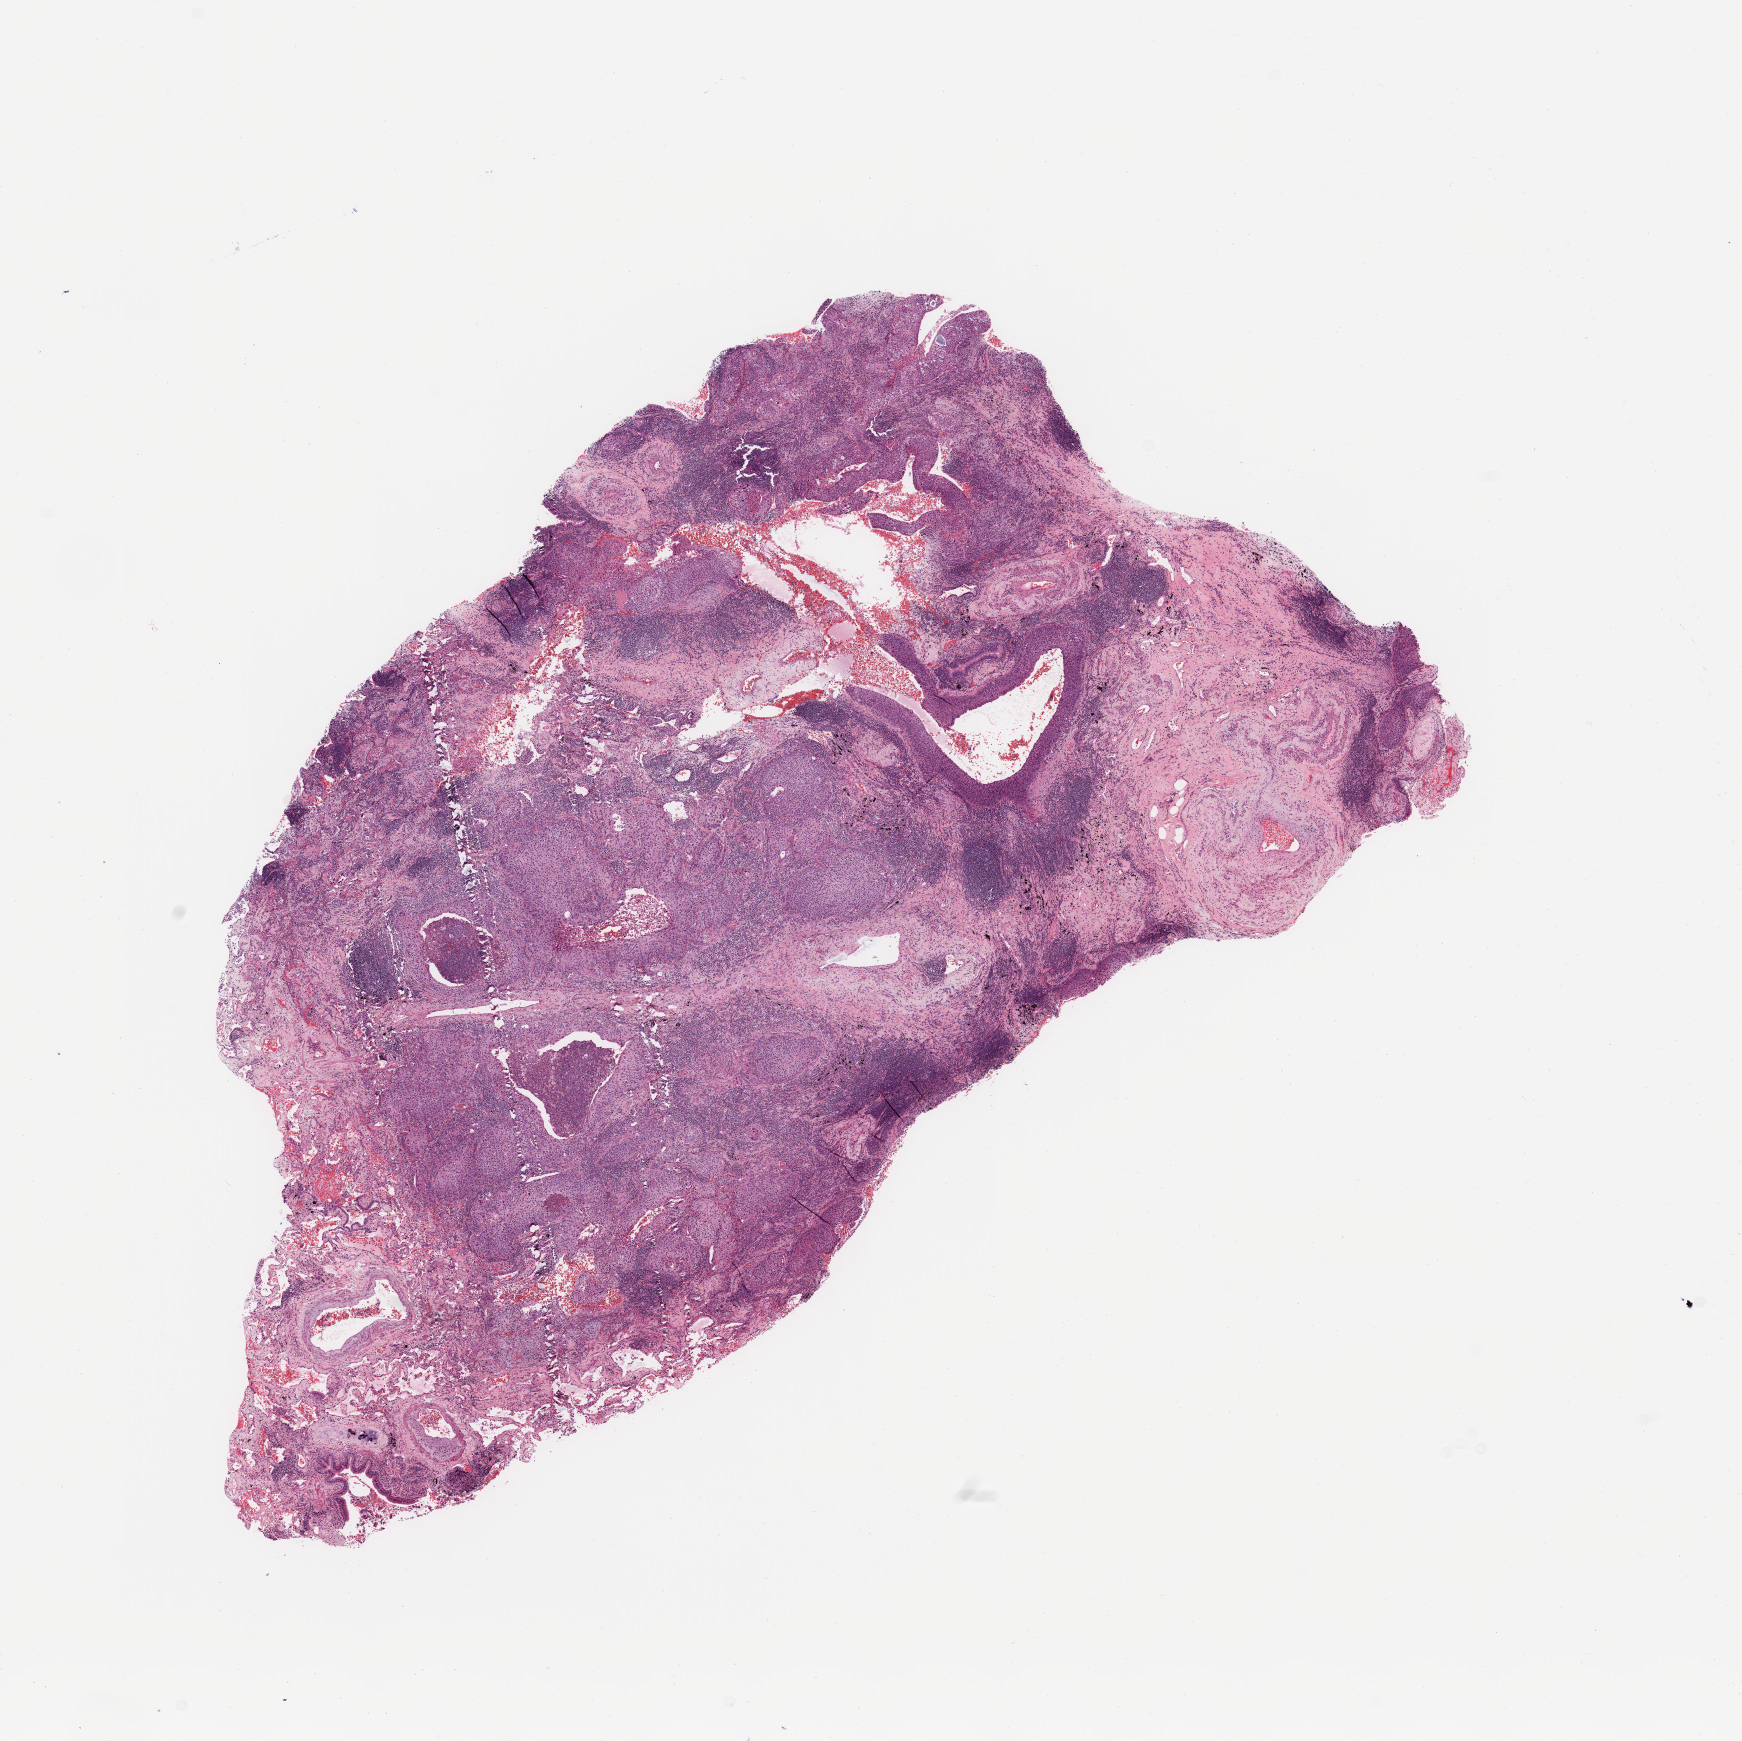
Whole-slide histology image, H&E-stained — shown as a low-resolution overview of the whole scanned area (about 13.8 x 13.8 mm), tumour tissue sample, sampled site: lung. 71-year-old female patient.
Diagnosis: Squamous cell carcinoma, NOS.